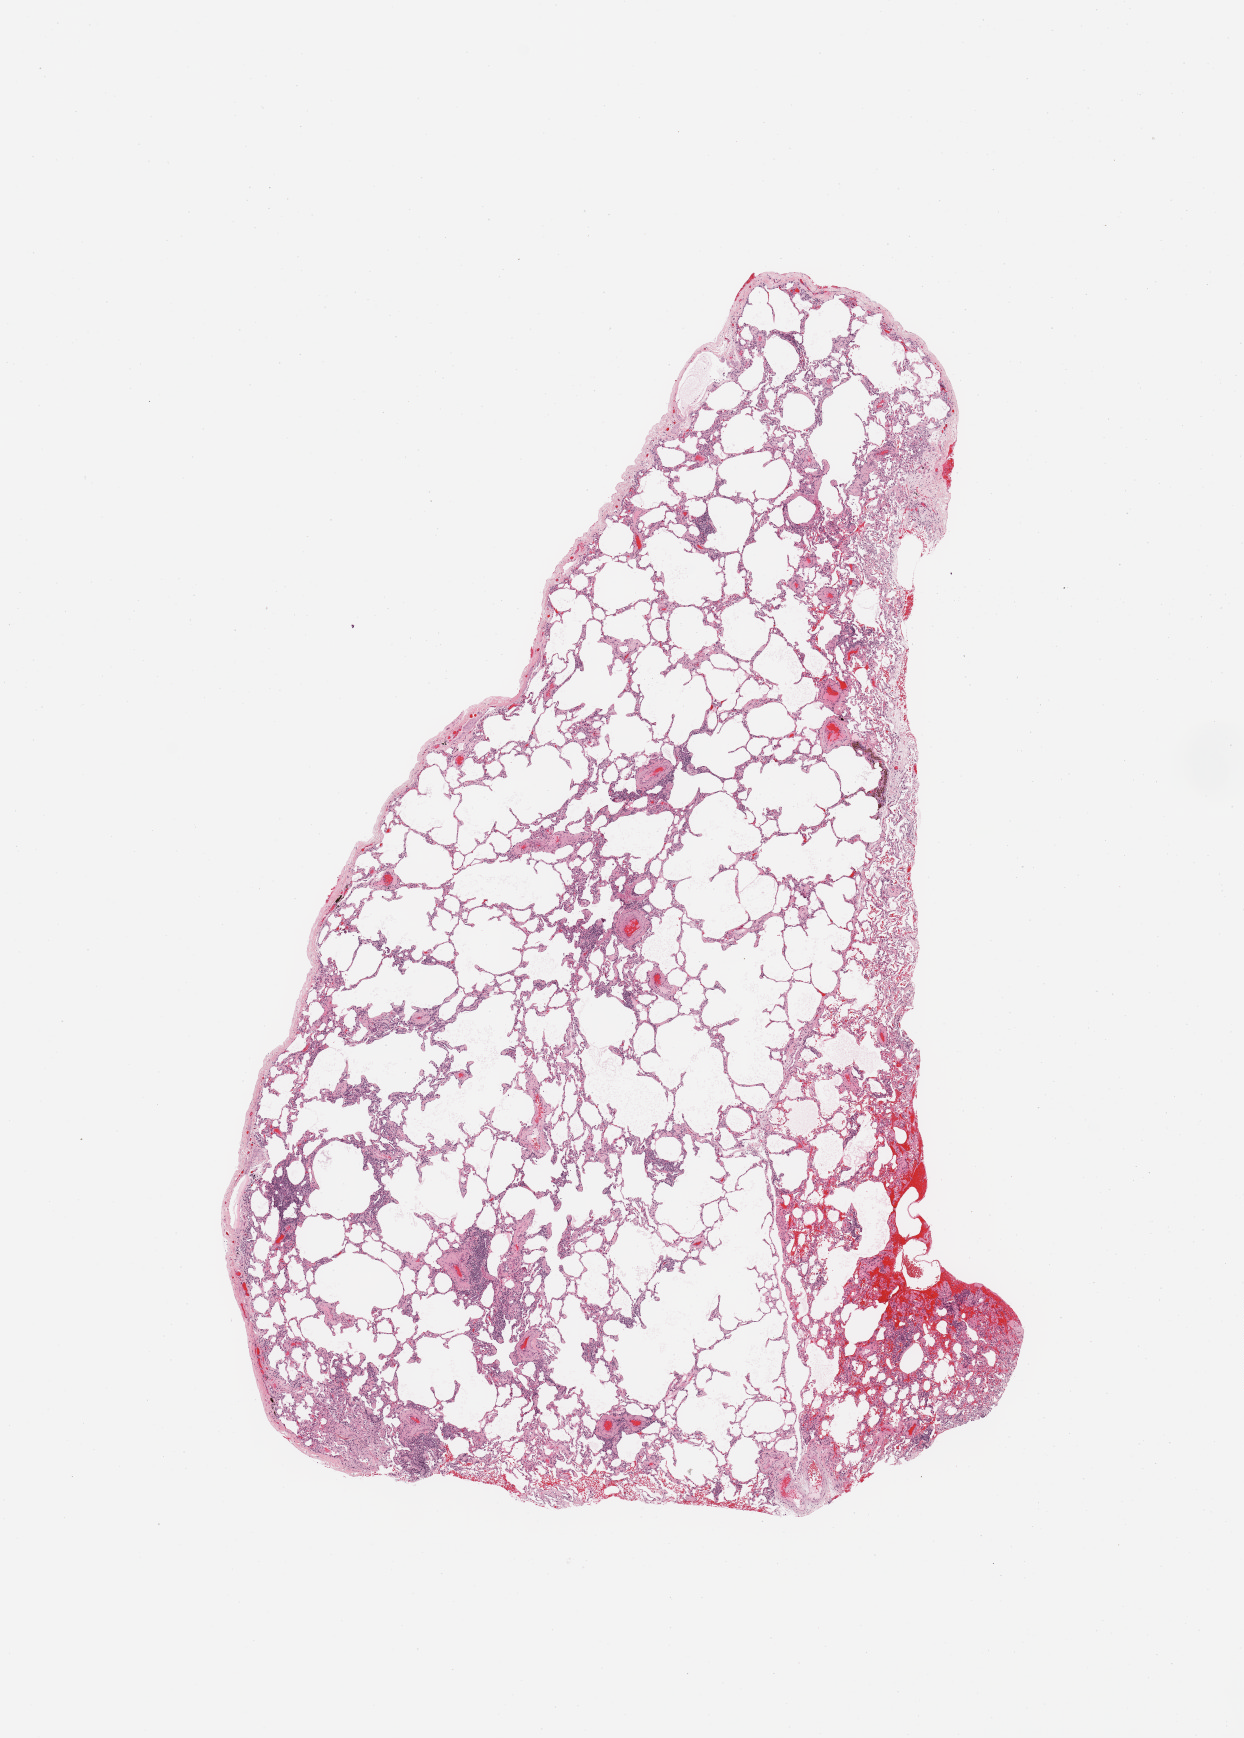
Whole-slide histology image, Hematoxylin and eosin (H&E) stained, a low-resolution overview of the entire scanned area, about 9.8 x 13.8 mm (acquisition: 20x scan). Normal (non-tumour) tissue sample, sampled site: lung. Patient: female, age 60 years.
• this section: normal (non-tumour) tissue from the same patient
• patient diagnosis: Adenocarcinoma, NOS